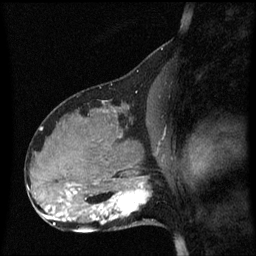
Breast MRI (dynamic contrast-enhanced), one sagittal slice; slice 29 of 60 in the series (ordered by position); dynamic contrast-enhanced series, image 2 of 3 at this slice position (ordered by acquisition); 1.5 T; TE 4.2 ms, TR 8.4 ms; 2.1 mm slice thickness; 256 × 256 image matrix, field of view 210 × 210 mm. Female patient, age 31 years. Case-level facts recorded for this patient, not image findings: setting: breast cancer imaged before/during neoadjuvant chemotherapy; receptor status: HR-positive, HER2-negative.
Outlined on this slice (semi-automatically segmented with operator editing):
- analysis volume of interest (the breast-tissue region the enhancement analysis was run in; not a lesion): box from (x=98, y=175) to (x=159, y=228) px
- tumour enhancement mask (voxels above the 70 % enhancement threshold inside the analysis volume of interest): (x=98, y=183)–(x=149, y=224)